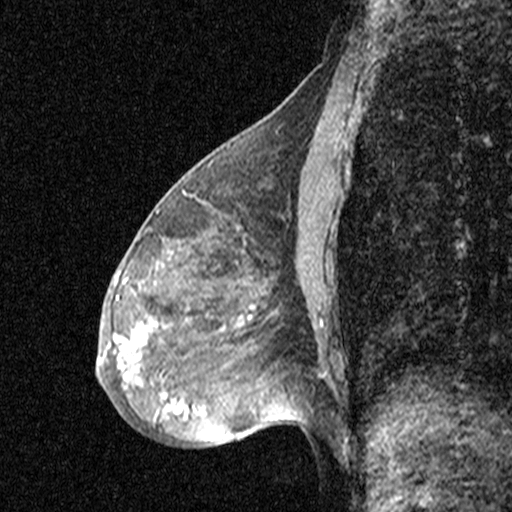
Breast MRI (dynamic contrast-enhanced), one sagittal slice; position 21 of 44 along the scan axis; dynamic contrast-enhanced study with each time point stored as its own series, time point 2 of 3 at this slice position (early post-contrast, ordered by acquisition time); 1.5 T; TE 4.5 ms, TR 11 ms; 3 mm slice thickness; 512 × 512 image matrix. Patient: female, 53 years. Case-level facts recorded for this patient, not image findings: setting: breast cancer imaged before/during neoadjuvant chemotherapy; receptor status: HR-positive, HER2-negative.
Structures marked on this image (semi-automatically segmented with operator editing):
- analysis volume of interest (the breast-tissue region the enhancement analysis was run in; not a lesion): bounding box (x1, y1, x2, y2) in pixels: (88, 176, 313, 423)
- tumour enhancement mask (voxels above the 90 % enhancement threshold inside the analysis volume of interest): (97, 331, 187, 418)